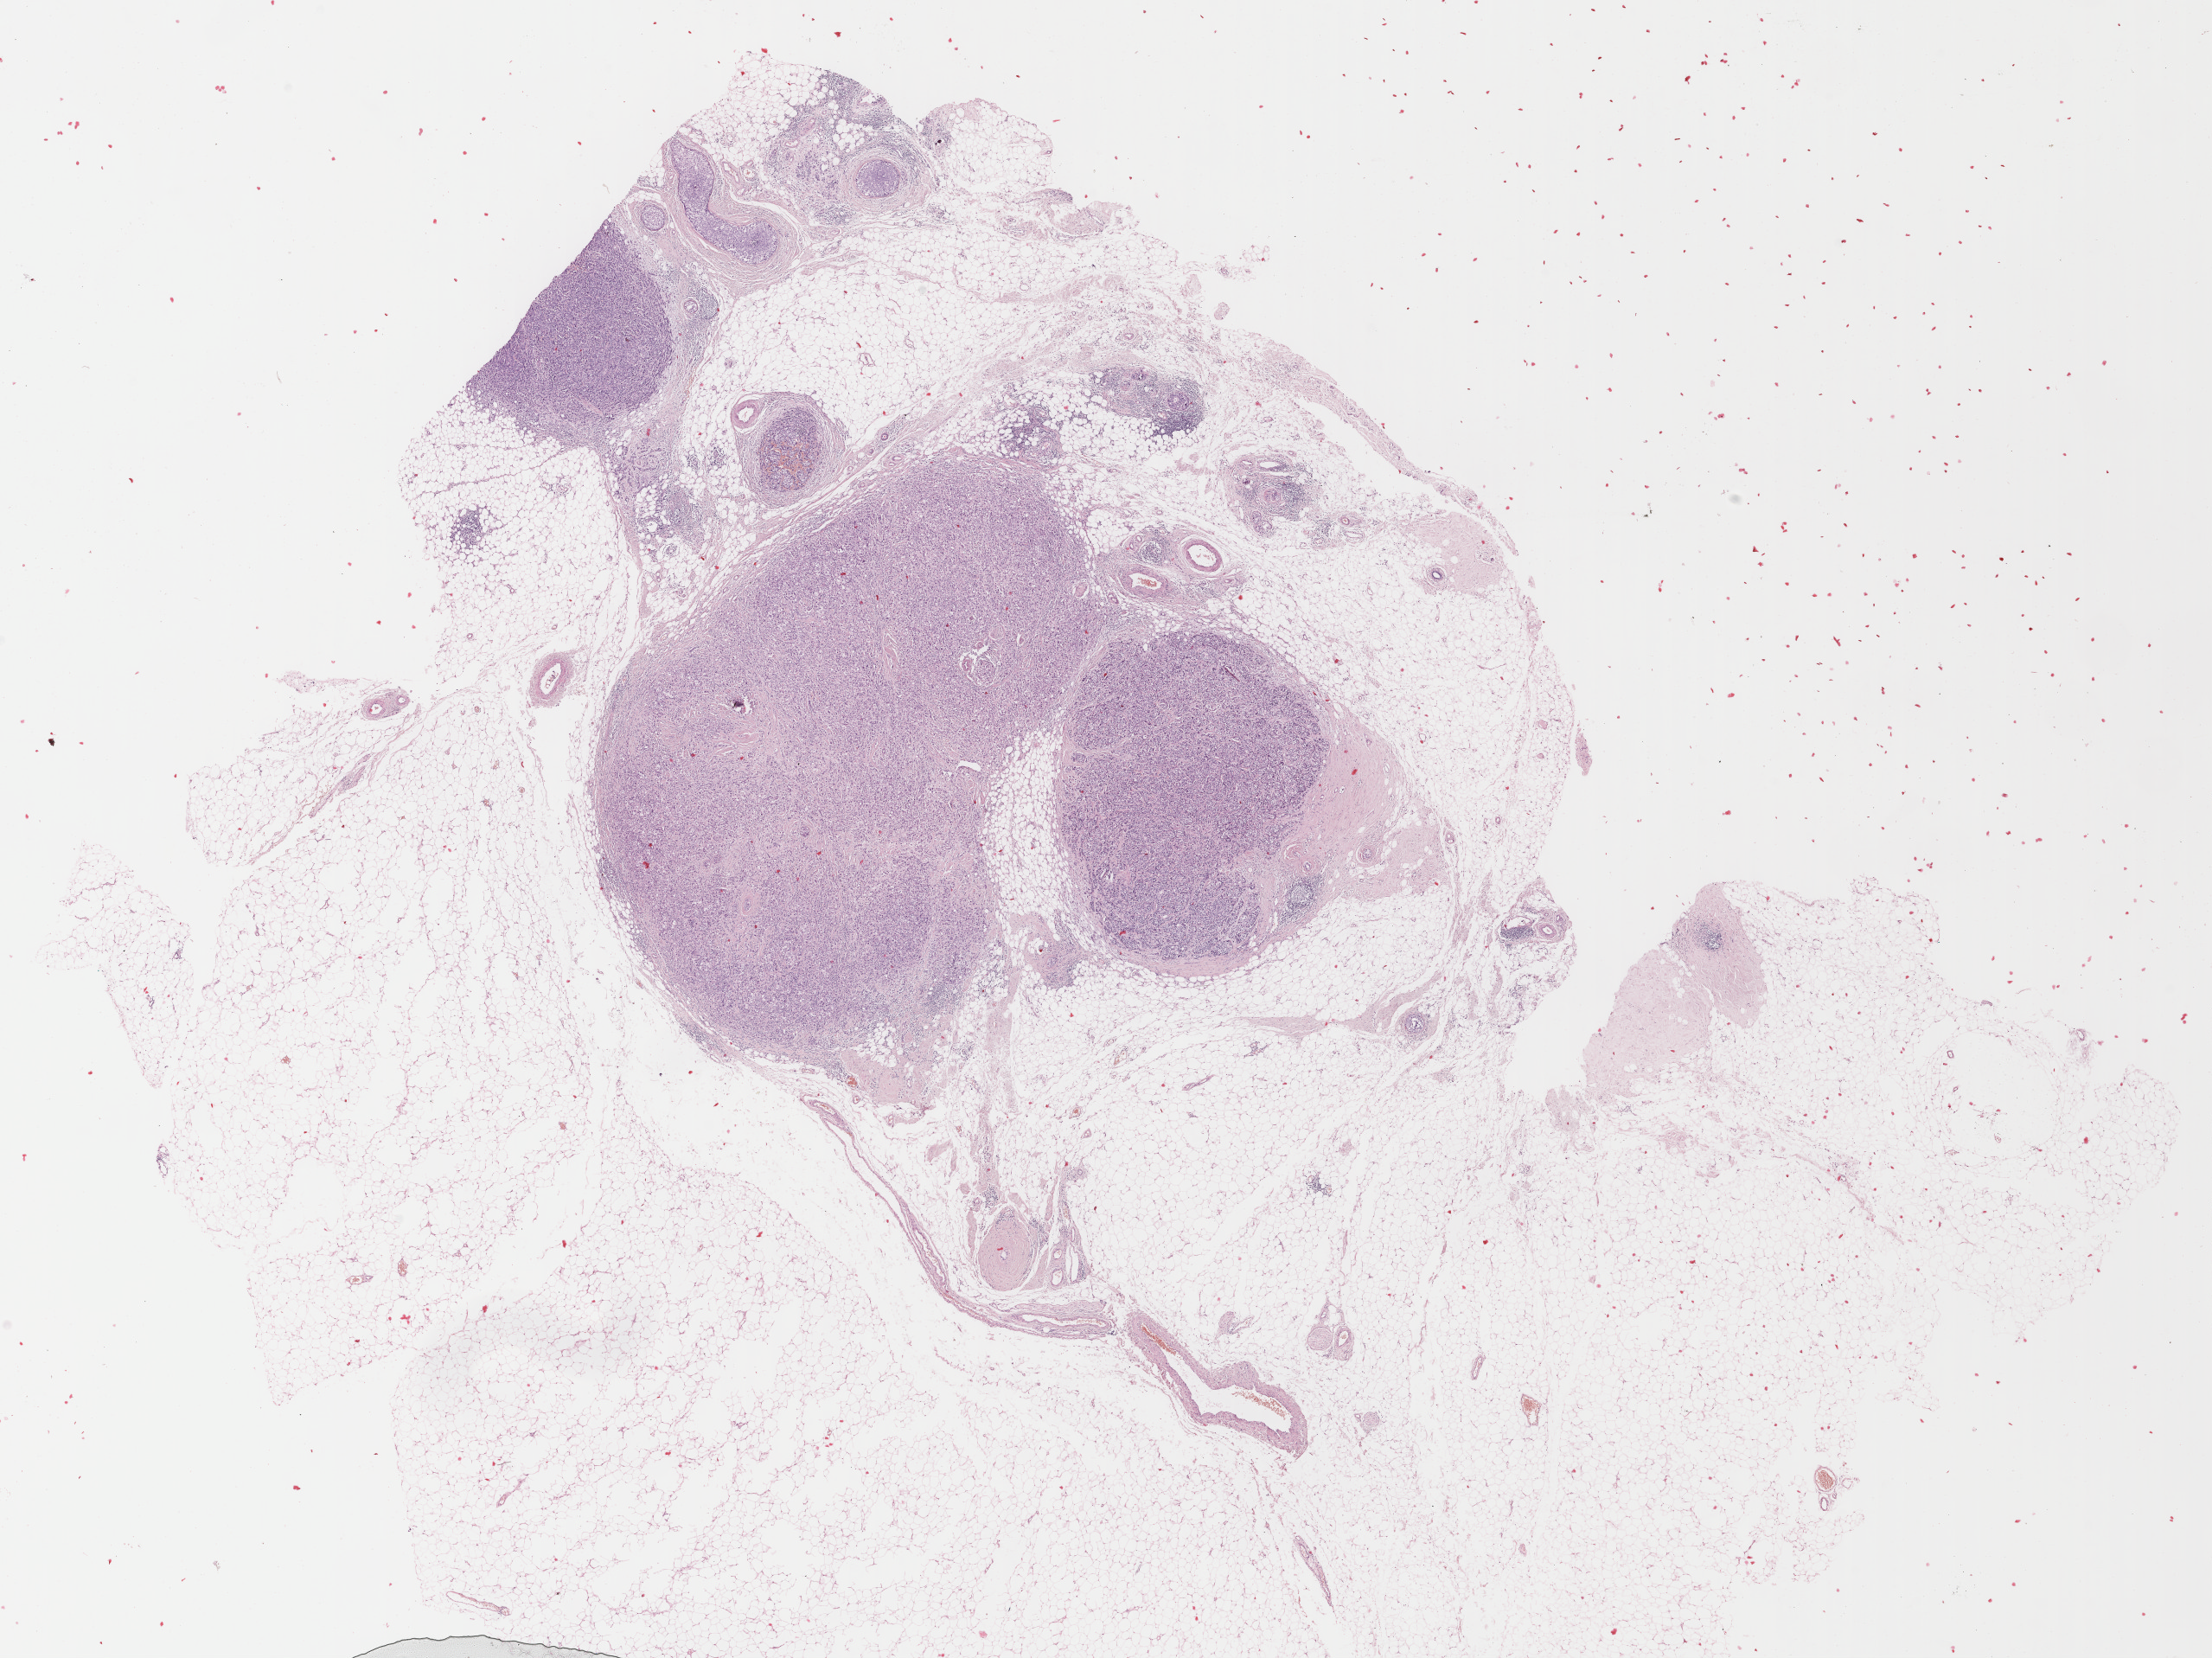
Digitized Hematoxylin and eosin (H&E) stained tissue section (whole slide) — whole scanned area (about 20.3 x 15.2 mm) shown as a low-resolution overview, formalin-fixed paraffin-embedded (FFPE) diagnostic section, sample: primary tumour, breast. Female, age 62 years at initial diagnosis.
- histologic diagnosis: Infiltrating duct carcinoma, NOS
- AJCC pathologic stage: IIB (7th edition)